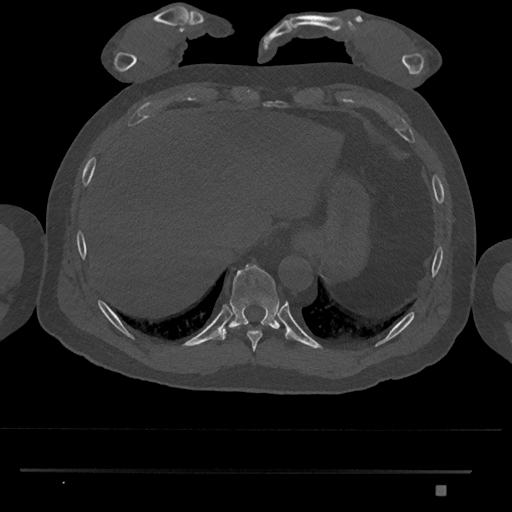
CT including the spine, one axial slice. Position 1023 of 1134 along the scan axis. Reconstruction kernel Br40s/3. 120 kVp. Bone window (W 1800 / L 400 HU). 0.5 mm slice thickness. 512 × 512 image matrix, field of view 429 × 429 mm. Male patient, age 65 years. Case-level facts recorded for this patient, not image findings: primary cancer: prostate.
Outlined on this slice (semi-automatic segmentation, software-assisted and operator-edited):
- T10 vertebra: box from (x=220, y=264) to (x=280, y=341) px
- T9 vertebra: (x=237, y=326)–(x=262, y=352)